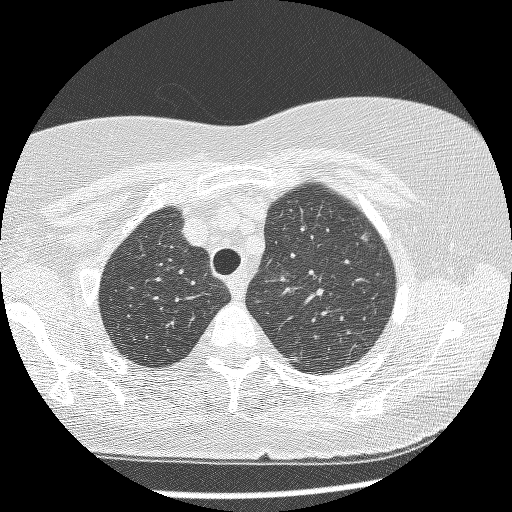
Chest CT (low-dose screening protocol), one axial image; first (baseline) screen; lung window (W 1500 / L -600 HU); 1.25 mm slice thickness. Female participant, aged 61 years at enrolment.
Expert reader's lesion annotation, bounding box [x1, y1, x2, y2] px = [329, 221, 385, 272]. The screening reader recorded 4 non-calcified nodules or masses ≥4 mm on this exam; which of them this box marks is not recorded.